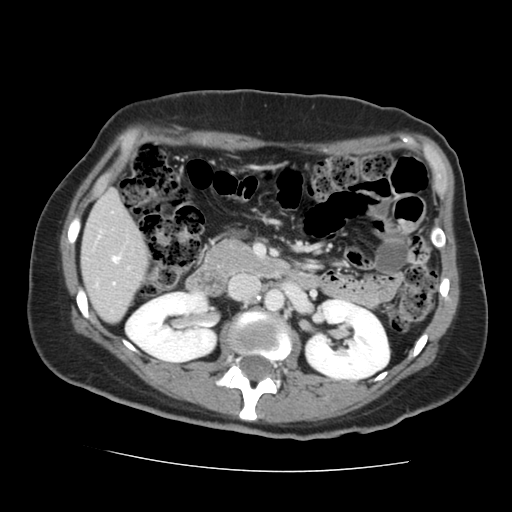
Contrast-enhanced abdominal CT, one axial slice. Position 63 of 144 along the scan axis. Intravenous contrast given. Soft-tissue window (W 400 / L 40 HU). 512 × 512 image matrix, field of view 333 × 333 mm. Female patient, age 46 years. Case-level facts recorded for this patient, not image findings: diagnosis: colorectal cancer liver metastases, imaged before liver resection; multiple liver metastases: no; largest metastasis: 2.8 cm; chemotherapy before resection: yes.
Structures marked on this image (outlined manually by an expert reader):
- liver: bounding box (x1, y1, x2, y2) in pixels: (83, 193, 146, 322)
- planned liver remnant (the part of the liver to remain after resection): (83, 193, 146, 322)
- portal vein (with intrahepatic branches): (112, 257, 120, 262)